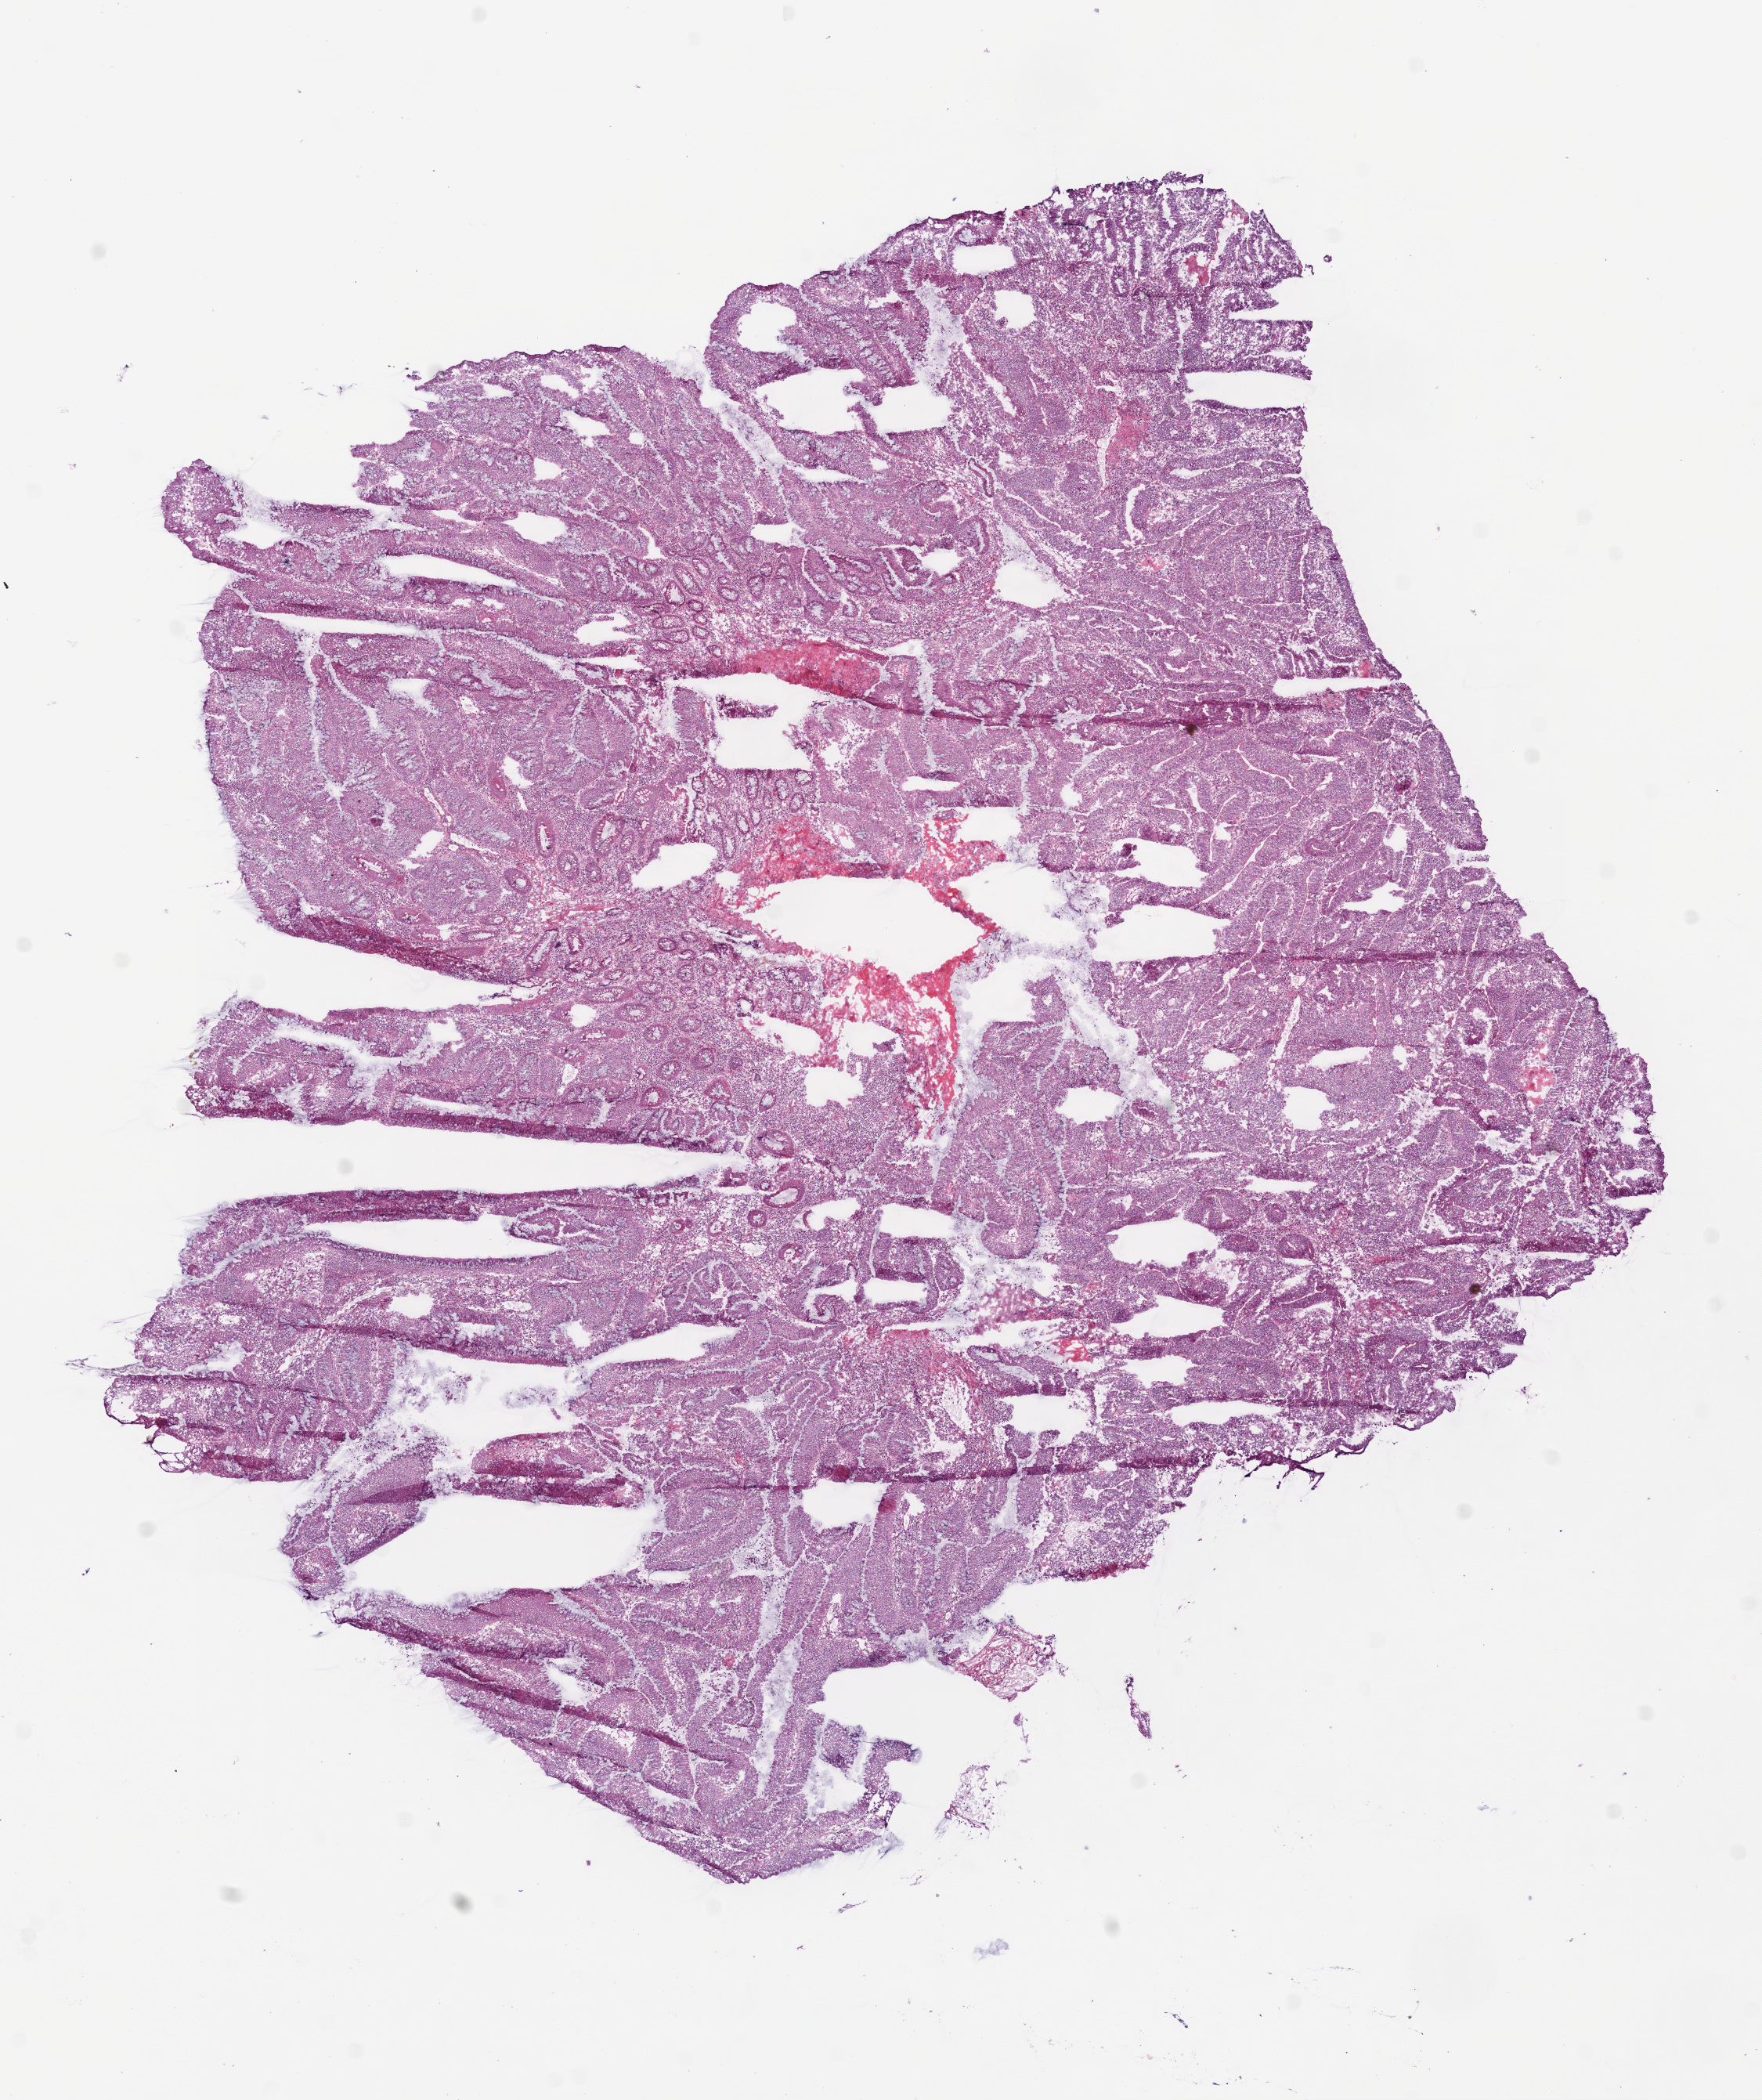
Whole-slide histology image, H&E, whole scanned area (about 9.0 x 10.8 mm) shown as a low-resolution overview. Frozen section. Sample: primary tumour, colon. Patient: male, age at initial diagnosis 72 years. Slide review estimates, as recorded: tumour cells 85%, tumour nuclei 80%, normal cells 8%, stromal cells 5%, necrosis 2%.
Lymph nodes positive (case pathology): 0 of 17 examined. Diagnosis: Adenocarcinoma, NOS (cecum). AJCC pathologic stage: IIA (6th edition).